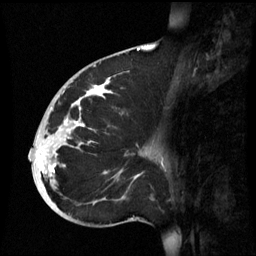
Breast MRI (dynamic contrast-enhanced), one sagittal slice; slice 28 of 60 in the series (ordered by position); dynamic contrast-enhanced series, image 2 of 3 at this slice position (ordered by acquisition); 1.5 T; TE 4.2 ms, TR 8.9 ms; 256 × 256 image matrix. Patient: female, 35 years. From the clinical record (not read from this slice): setting: breast cancer imaged before/during neoadjuvant chemotherapy; receptor status: HR-positive, HER2-negative.
Outlined on this slice (semi-automatically segmented with operator editing):
- analysis volume of interest (the breast-tissue region the enhancement analysis was run in; not a lesion): bounding box (x1, y1, x2, y2) in pixels: (32, 74, 164, 221)
- tumour enhancement mask (voxels above the 70 % enhancement threshold inside the analysis volume of interest): (37, 78, 111, 179)